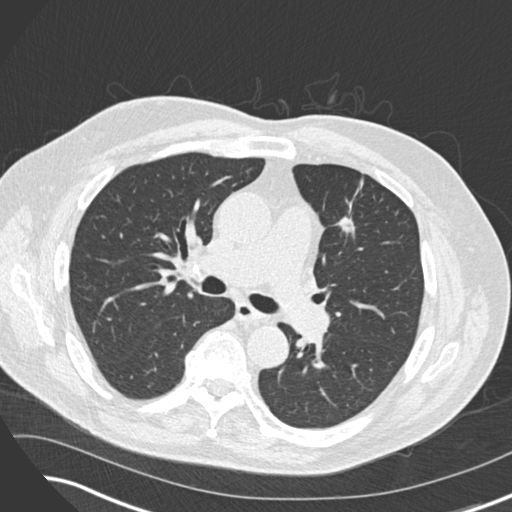
Low-dose screening chest CT, one axial slice; position 99 of 169 along the scan axis; reconstruction kernel B30f; 120 kVp; lung window (W 1500 / L -600 HU); 2 mm slice thickness; 512 × 512 image matrix, field of view 360 × 360 mm.
Structures marked on this image (outlined manually by an expert reader):
- lesion 1 (tumor, upper lobe of left lung): bounding box <336,217,355,233> (left, top, right, bottom; pixels)